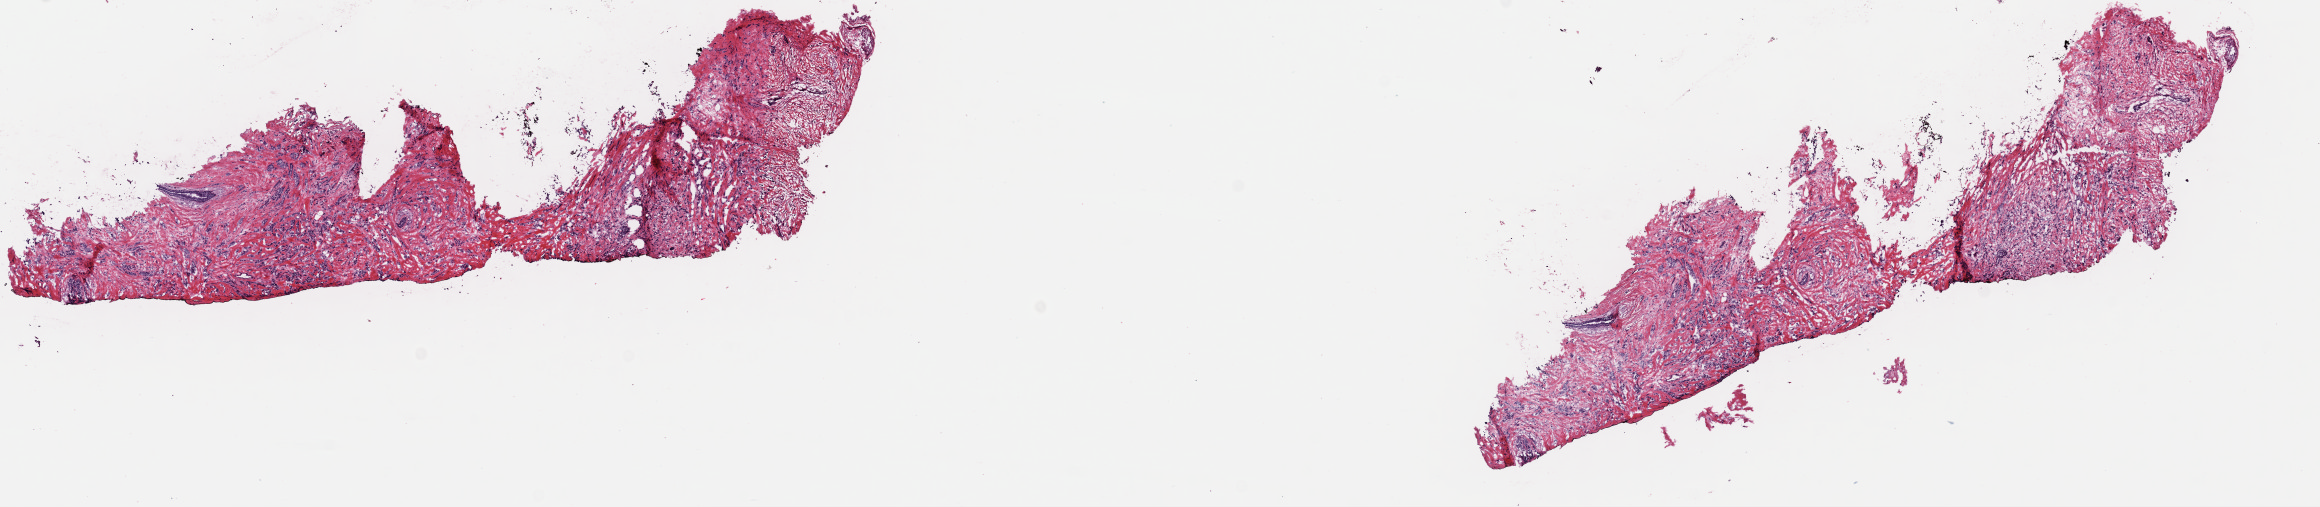
Whole-slide histology image, Hematoxylin and eosin (H&E) stained — shown as a low-resolution overview of the whole scanned area (about 18.3 x 4.0 mm, acquisition: 40x scan); frozen section from the top of the tissue portion; breast, primary tumour sample. Female, age 71 years at initial diagnosis. Composition of this section per pathologist review: tumour cells 70%, tumour nuclei 70%, normal cells 5%, stromal cells 25%, necrosis 0%. Inflammatory infiltration, as recorded: lymphocyte infiltration 0%, monocyte infiltration 0%, neutrophil infiltration 0%.
* TNM: T3 N1a MX
* laterality: left
* AJCC pathologic stage: IIIA
* pathologic diagnosis: Lobular carcinoma, NOS